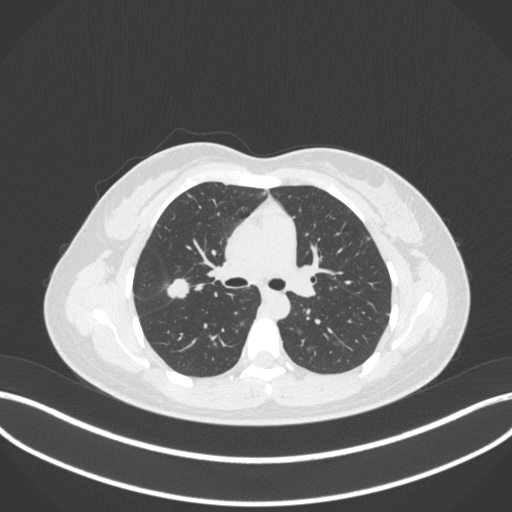
Chest CT, one axial slice. Position 208 of 214 along the scan axis. Reconstruction kernel B31f. 120 kVp. Lung window (W 1500 / L -600 HU). 1 mm slice thickness. 512 × 512 image matrix, field of view 400 × 400 mm. Female patient, age 33 years. Case-level facts recorded for this patient, not image findings: clinical TNM (as recorded): T1c N0 M0; histopathological grade: G2-G3.
Structures marked on this image (rectangle marked by the reading radiologist):
- lung tumour (recorded histology: adenocarcinoma): bounding box [x1, y1, x2, y2] px = [162, 275, 198, 304]